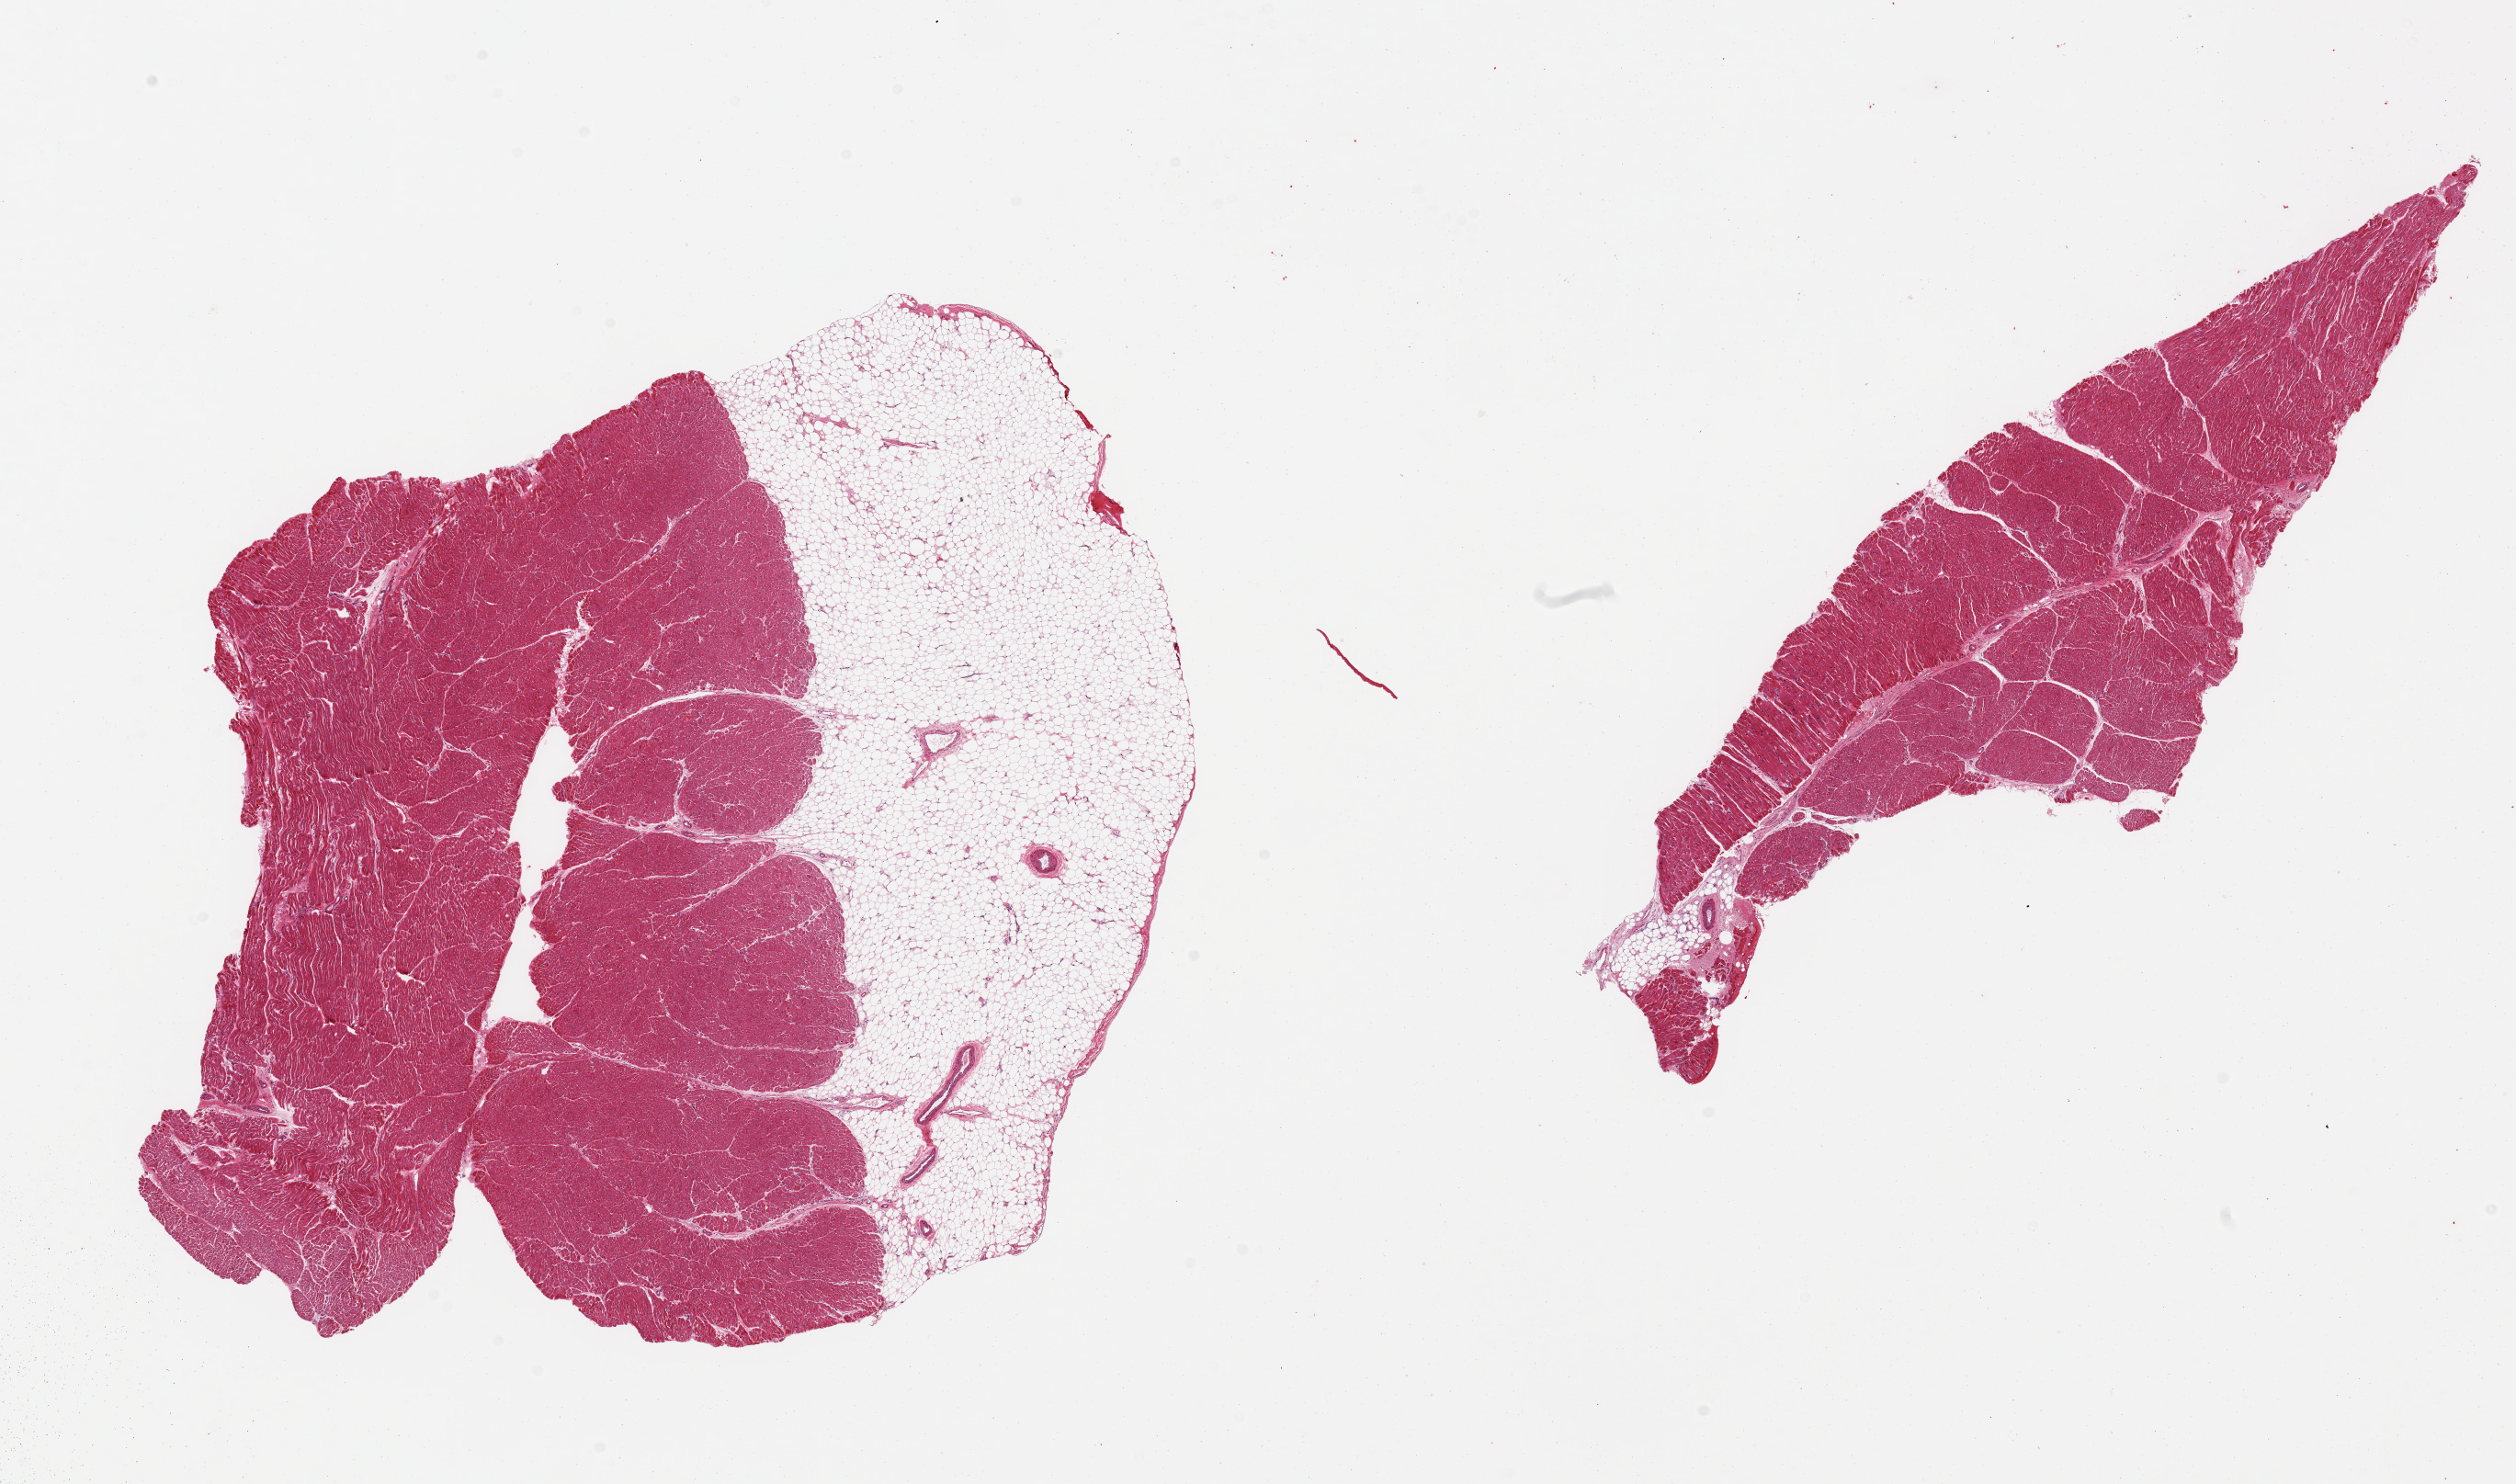
Digitized haematoxylin and eosin-stained section, a low-resolution overview of the entire scanned area, about 21.7 x 12.8 mm (from a 20x scan), PAXgene-fixed paraffin-embedded (PFPE) section, target tissue: auricular appendage, tissue donor sample. Male donor.
* reviewer comment on this tissue sample: 2 pieces; 40% external fat on 1; muscle resembles ventricular myocardium rather than atrial